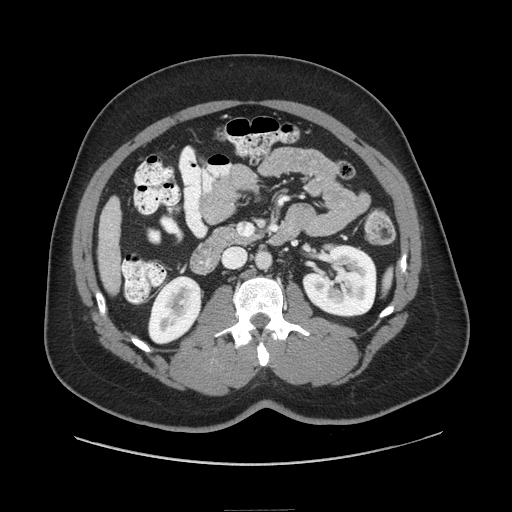
Contrast-enhanced abdominal CT (liver protocol), one axial slice. Position 19 of 87 along the scan axis. Reconstruction kernel STANDARD. 140 kVp. Soft-tissue window (W 400 / L 40 HU). 2.5 mm slice thickness. 512 × 512 image matrix, field of view 440 × 440 mm. From the clinical record (not read from this slice): diagnosis: hepatocellular carcinoma (patient treated with transarterial chemoembolisation; whether this scan precedes or follows treatment is not stated here); TNM stage (as recorded): Stage-II; Child-Pugh class: A; tumour differentiation: moderately differentiated.
Outlined on this slice (semi-automatically segmented with operator editing):
- liver parenchyma outside the tumour (the mass and vessels are separate outlines, so this box may not span the whole liver): box from (x=98, y=197) to (x=120, y=294) px